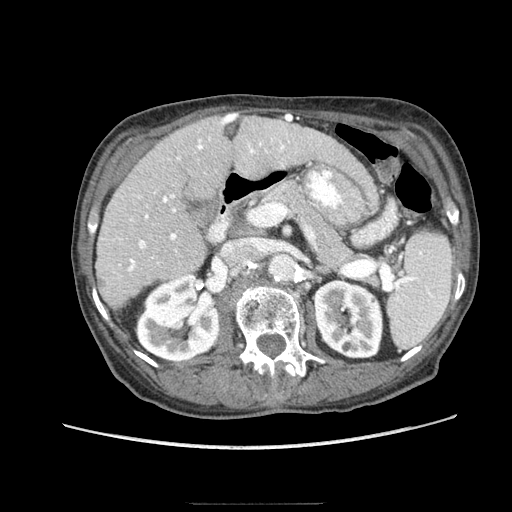
Contrast-enhanced abdominal CT (liver protocol), one axial slice. Reconstruction kernel STANDARD. 140 kVp. Soft-tissue window (W 400 / L 40 HU). 2.5 mm slice thickness. 512 × 512 image matrix. From the clinical record (not read from this slice): diagnosis: hepatocellular carcinoma (patient treated with transarterial chemoembolisation; whether this scan precedes or follows treatment is not stated here); TNM stage (as recorded): Stage-I; Child-Pugh class: A; tumour differentiation: moderately differentiated.
Outlined on this slice (semi-automatically segmented with operator editing):
- liver parenchyma outside the tumour (the mass and vessels are separate outlines, so this box may not span the whole liver): bounding box <96,114,349,308> (left, top, right, bottom; pixels)
- liver vessels: <128,114,288,272>